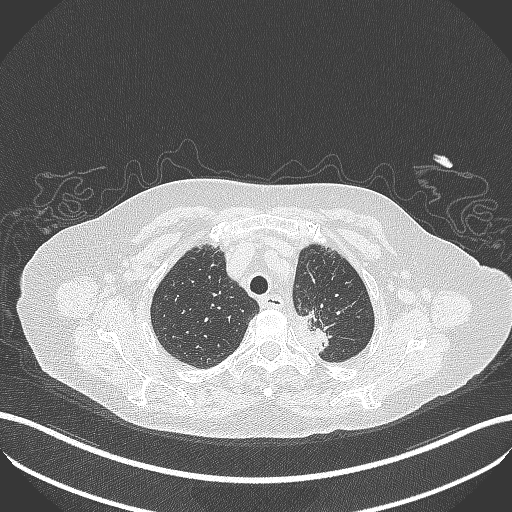
Chest CT, one axial slice. 100 kVp. Lung window (W 1500 / L -600 HU). 1 mm slice thickness. 512 × 512 image matrix, field of view 400 × 400 mm. Female patient, age 81 years. From the clinical record (not read from this slice): clinical TNM (as recorded): T2a N0 M0.
Annotated regions visible in this slice (bounding box drawn by a radiologist):
- lung tumour (recorded histology: adenocarcinoma): box from (x=292, y=311) to (x=335, y=359) px